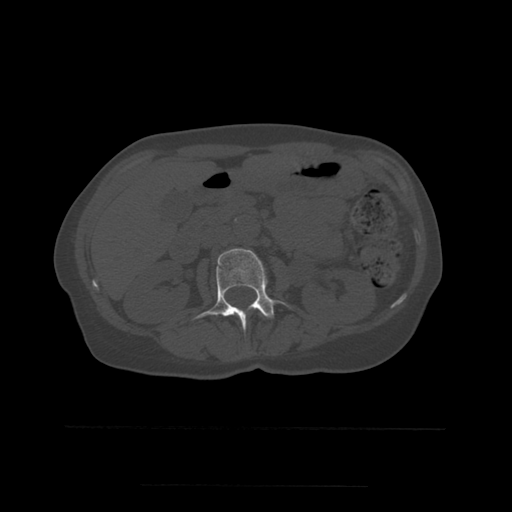
CT including the spine, one axial slice. Position 215 of 544 along the scan axis. Bone window (W 1800 / L 400 HU). 1.25 mm slice thickness. 512 × 512 image matrix. Patient age 58 years. From the clinical record (not read from this slice): primary cancer: lung.
Outlined on this slice (semi-automatic segmentation, software-assisted and operator-edited):
- L1 vertebra: bounding box <260,312,263,315> (left, top, right, bottom; pixels)
- L2 vertebra: <194,248,285,331>